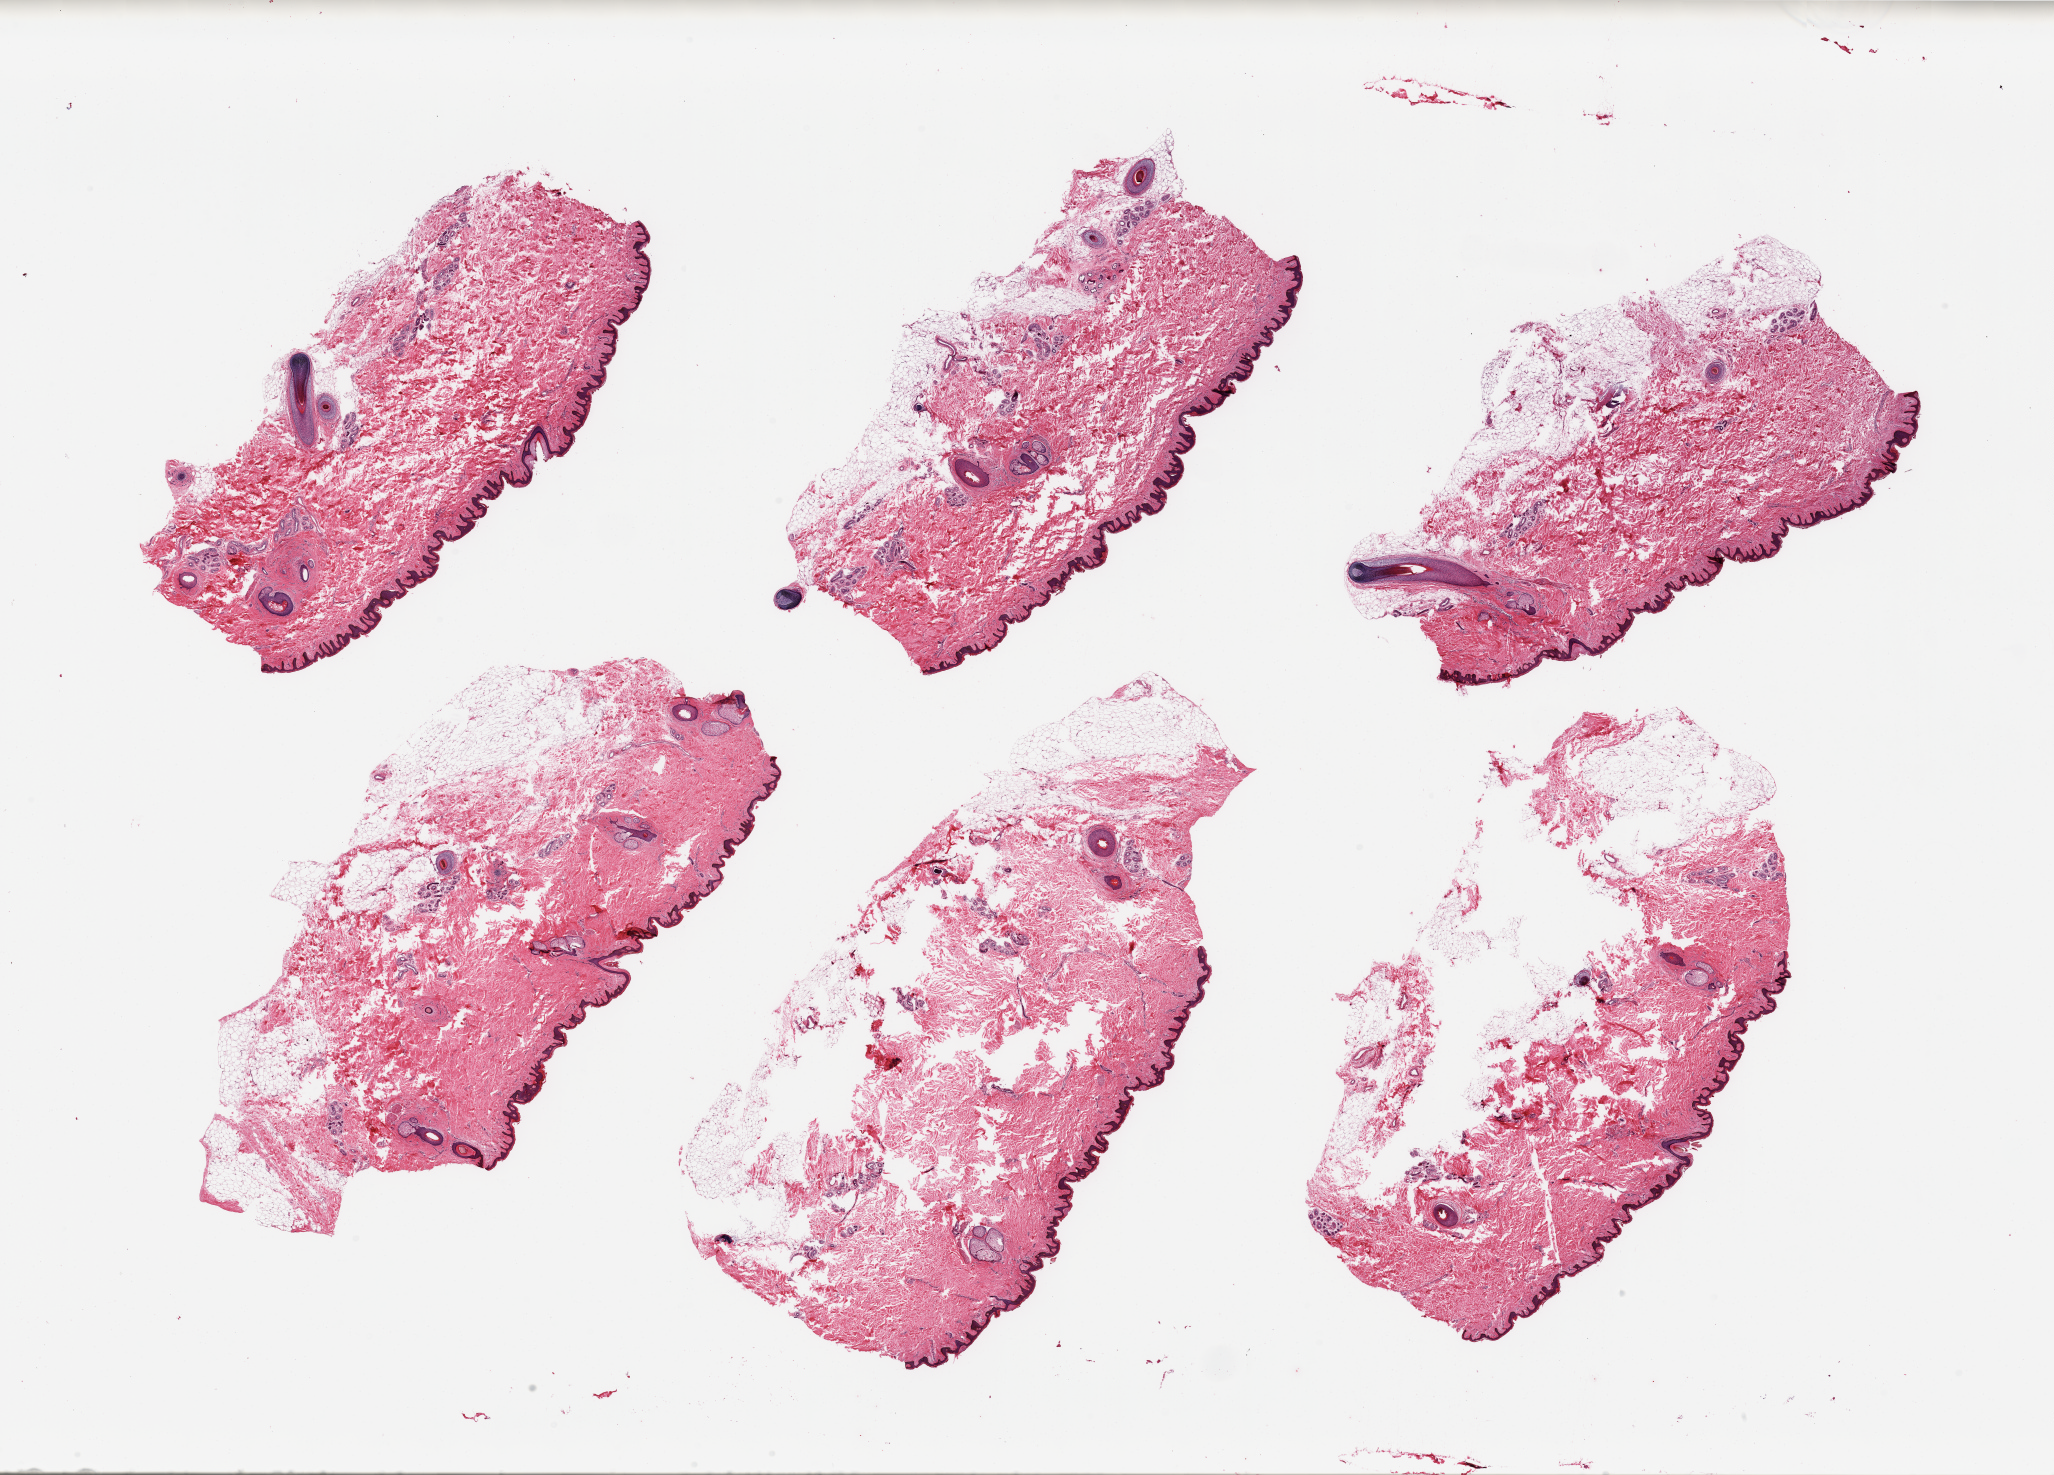
Whole-slide image, H&E stain, brightfield, shown as a low-resolution overview of the whole scanned area (about 32.5 x 23.3 mm). PAXgene-fixed, paraffin-embedded tissue. Section of skin of suprapubic region (target tissue). Donor tissue sample. Male donor.
* reviewer comment on this tissue sample: 6 pieces; partially fragmented hair-bearing skin with deep fat up to 1.7mm thick